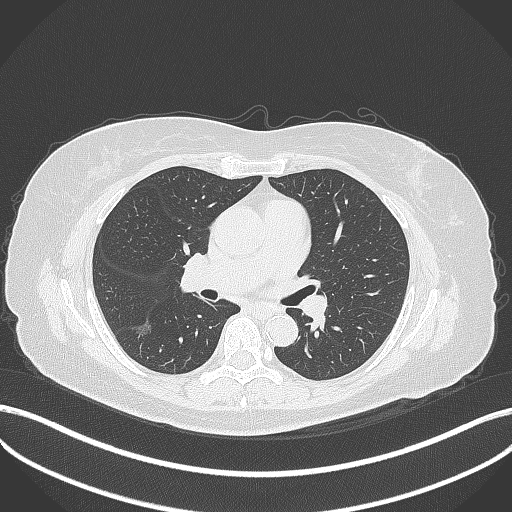
Chest CT, one axial slice; position 179 of 322 along the scan axis; reconstruction kernel B70f; lung window (W 1500 / L -600 HU); 1 mm slice thickness; 512 × 512 image matrix. Patient: female, 64 years. From the clinical record (not read from this slice): clinical TNM (as recorded): T1c N0 M0.
Outlined on this slice (rectangle marked by the reading radiologist):
- lung tumour (recorded histology: adenocarcinoma): box from (x=129, y=318) to (x=155, y=341) px